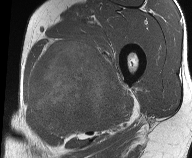
MRI of an extremity soft-tissue mass, one axial slice. Slice 31 of 61 in the series (ordered by position). MR volume resampled by the dataset authors to the PET/CT grid (not the native acquisition matrix). 3.27 mm slice thickness. 192 × 158 image matrix, field of view 187 × 154 mm. Male patient. From the clinical record (not read from this slice): histological type: pleiomorphic liposarcoma; grade: high; site of the primary tumour: left thigh.
Structures marked on this image (expert contour drawn on MRI and transferred to this co-registered scan by the dataset authors):
- gross tumour volume including surrounding oedema: box from (x=27, y=39) to (x=124, y=136) px
- gross tumour volume (mass): (x=29, y=41)–(x=122, y=127)